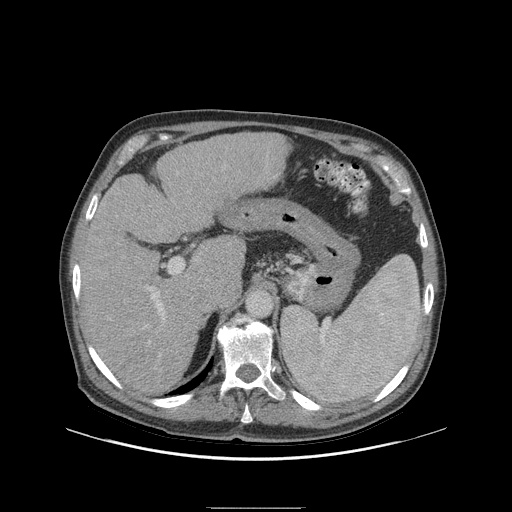
Contrast-enhanced abdominal CT (liver protocol), one axial slice. Position 61 of 105 along the scan axis. Reconstruction kernel STANDARD. 140 kVp. Soft-tissue window (W 400 / L 40 HU). 512 × 512 image matrix. Case-level facts recorded for this patient, not image findings: diagnosis: hepatocellular carcinoma (patient treated with transarterial chemoembolisation; whether this scan precedes or follows treatment is not stated here); TNM stage (as recorded): Stage-I; Child-Pugh class: A; tumour nodularity: uninodular.
Structures marked on this image (semi-automatically segmented with operator editing):
- liver parenchyma outside the tumour (the mass and vessels are separate outlines, so this box may not span the whole liver): box from (x=80, y=134) to (x=286, y=394) px
- liver vessels: (x=148, y=271)–(x=180, y=343)